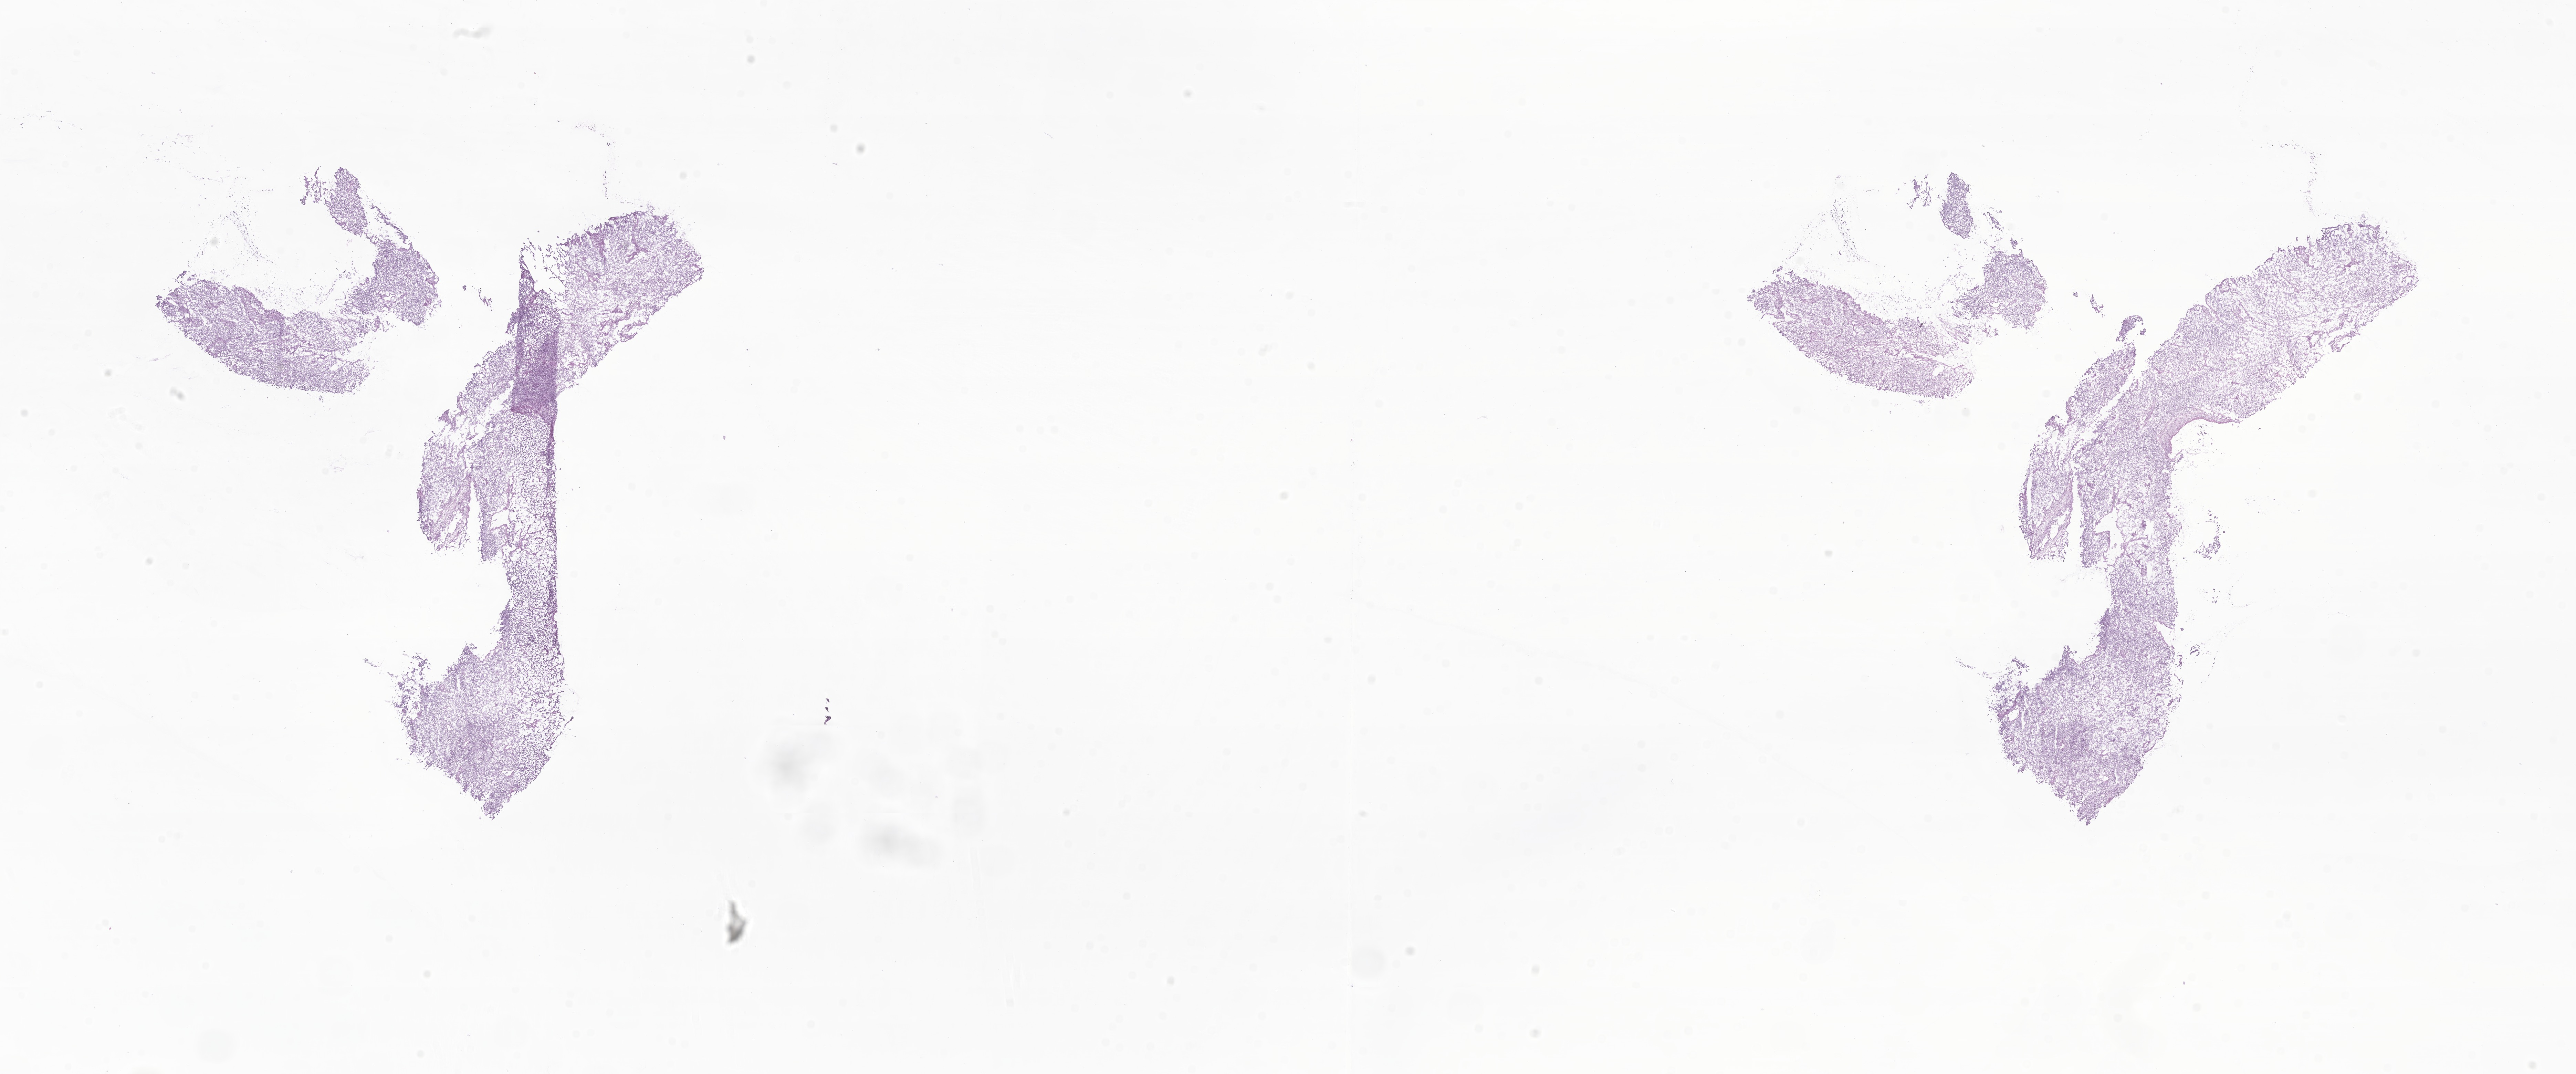
Digitized H&E-stained section of tumor tissue from the testis — whole scanned area (about 31.5 x 13.1 mm) shown as a low-resolution overview. Frozen section. Patient: male, age 89 months (7 years 5 months).
Recorded diagnosis: Embryonal rhabdomyosarcoma, NOS.